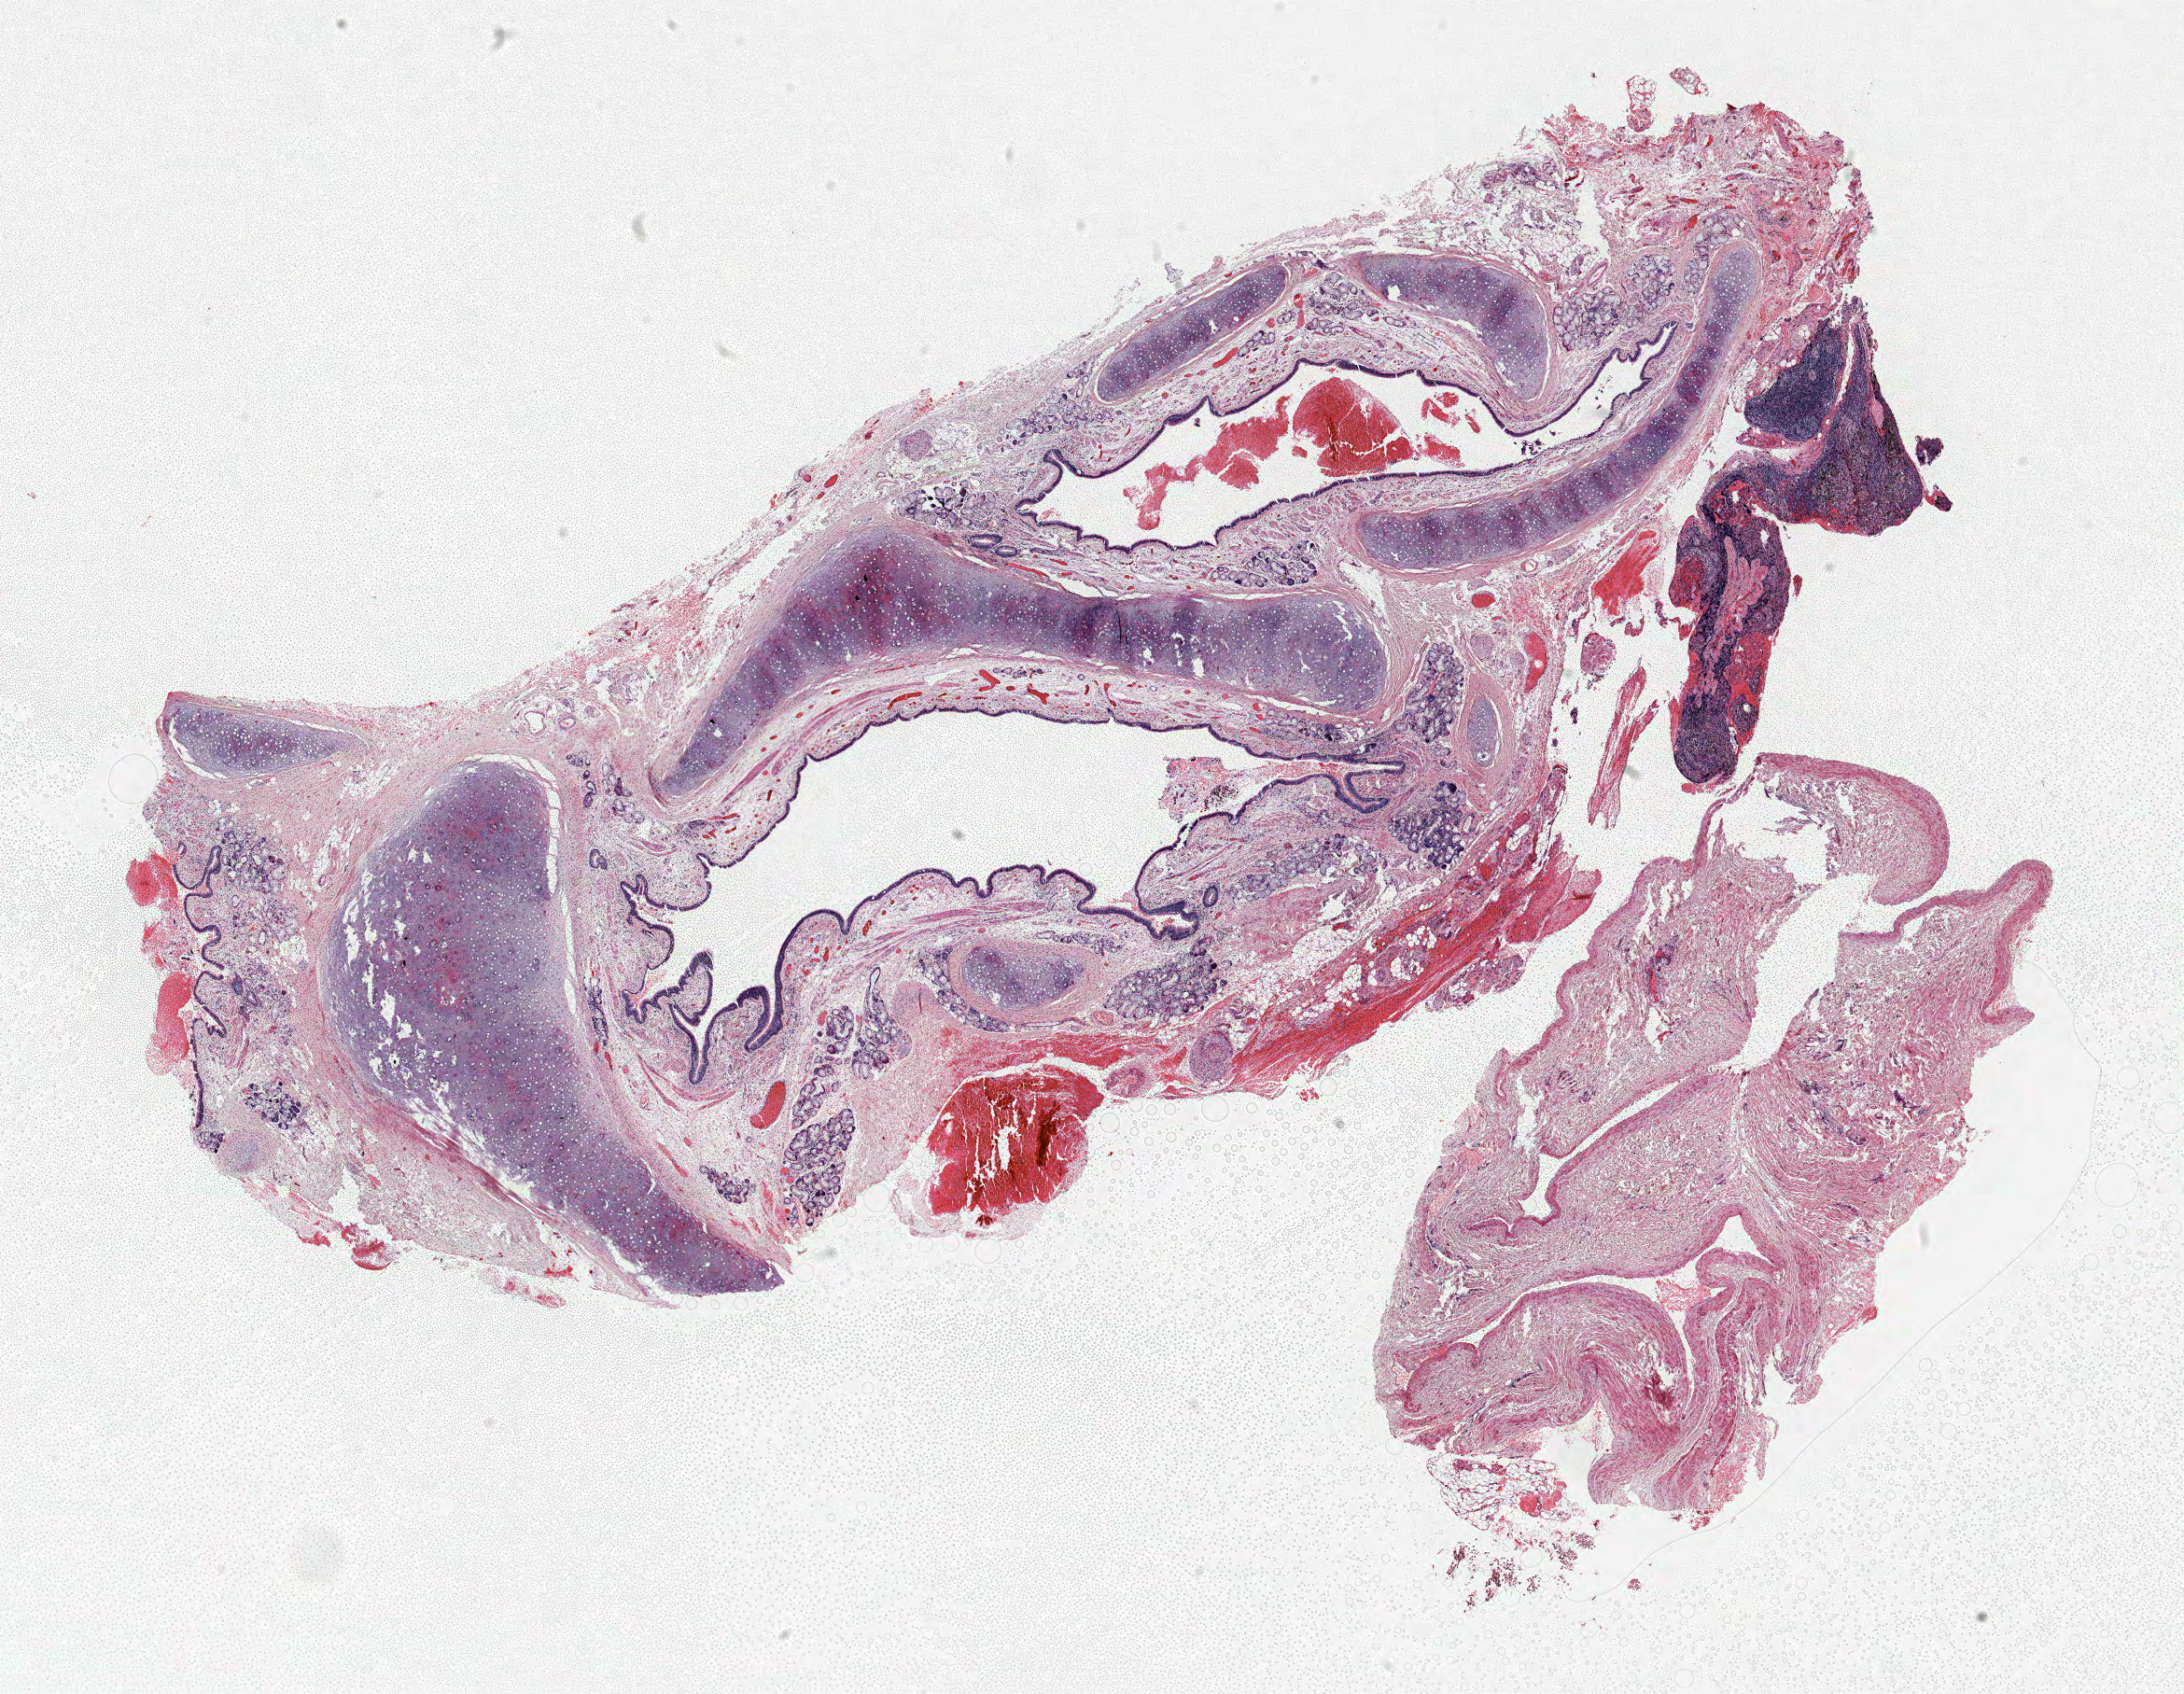
Hematoxylin and eosin (H&E) stained whole-slide image, a low-resolution overview of the entire scanned area, about 18.7 x 14.5 mm, FFPE section, lung. Female, age 57 at enrolment. Grade: moderately differentiated (G2).
Participant's lung-cancer diagnosis: Adenocarcinoma, NOS (ICD-O-3 8140/3). Stage (AJCC 6th edition): IA. Tumour size (pathology): 8 mm. Primary tumour location (clinical record): right lower lobe.